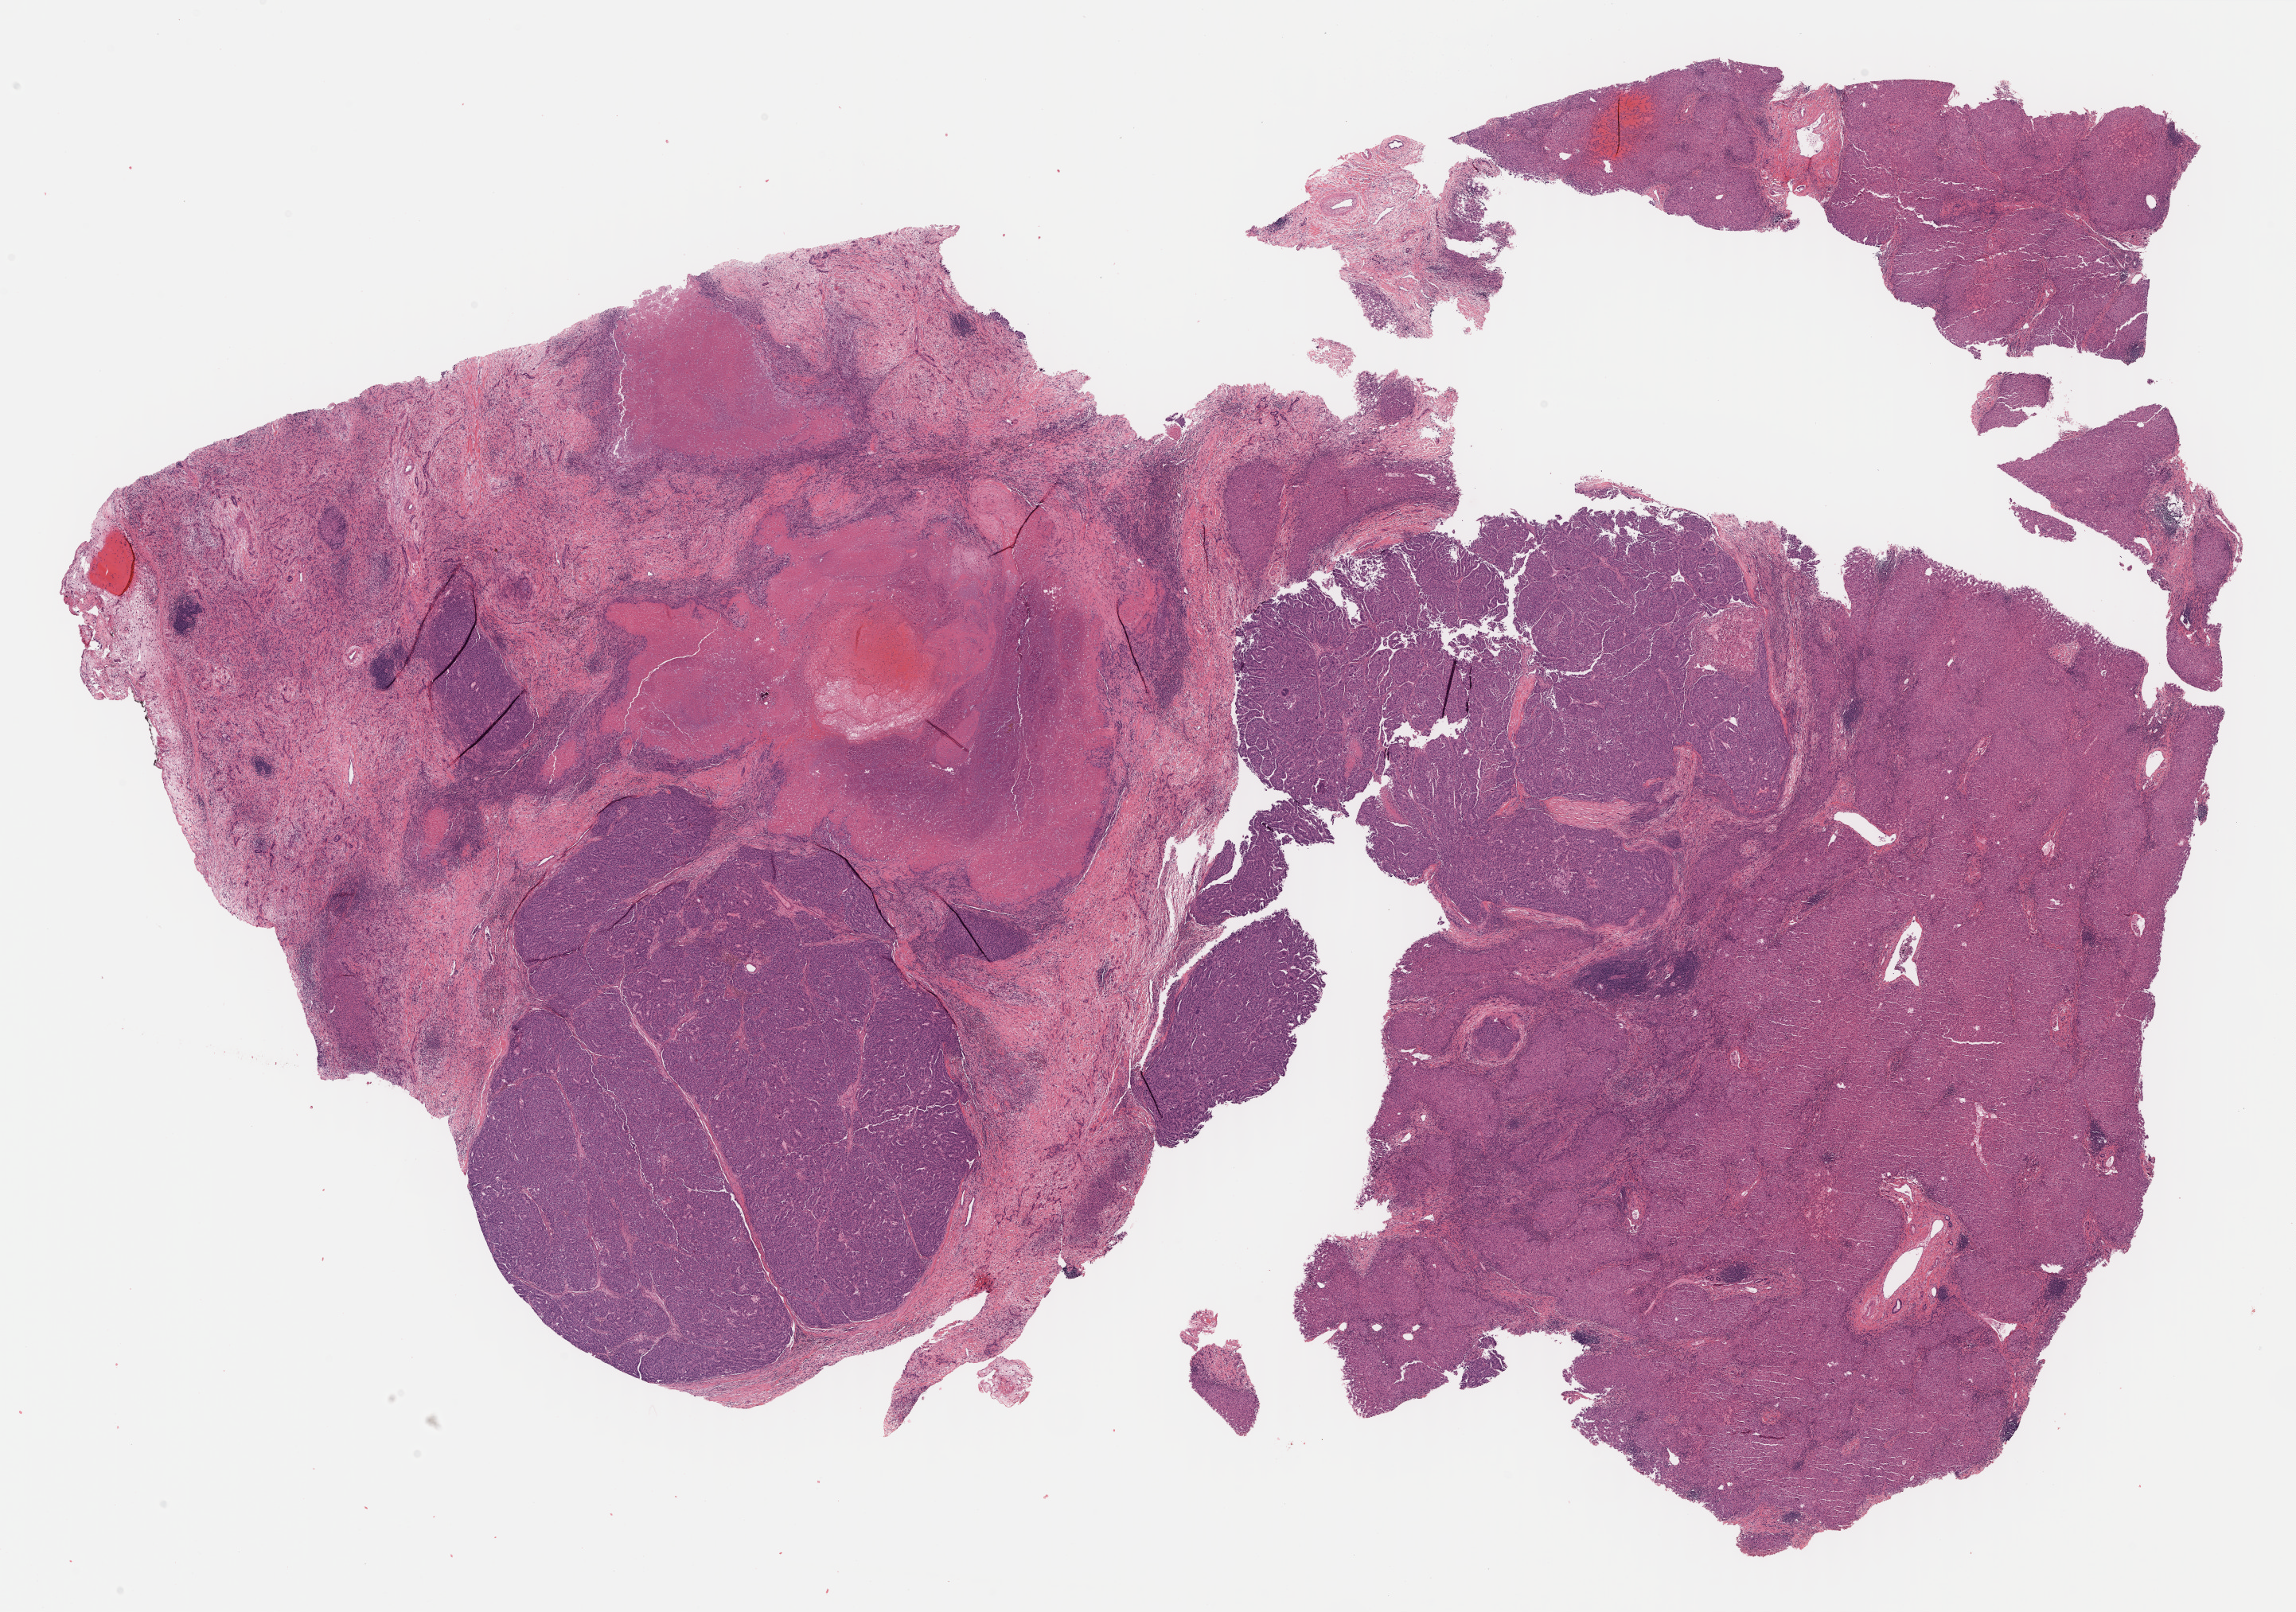
H&E whole-slide image, whole scanned area (about 23.4 x 16.4 mm, slide scanned at 40x) shown as a low-resolution overview, formalin-fixed paraffin-embedded (FFPE) diagnostic section, liver, primary tumour sample. Patient: male, age at initial diagnosis 42 years. Histologic grade: G3 (poorly differentiated).
AJCC pathologic stage: II. Histologic diagnosis: Hepatocellular carcinoma, NOS.